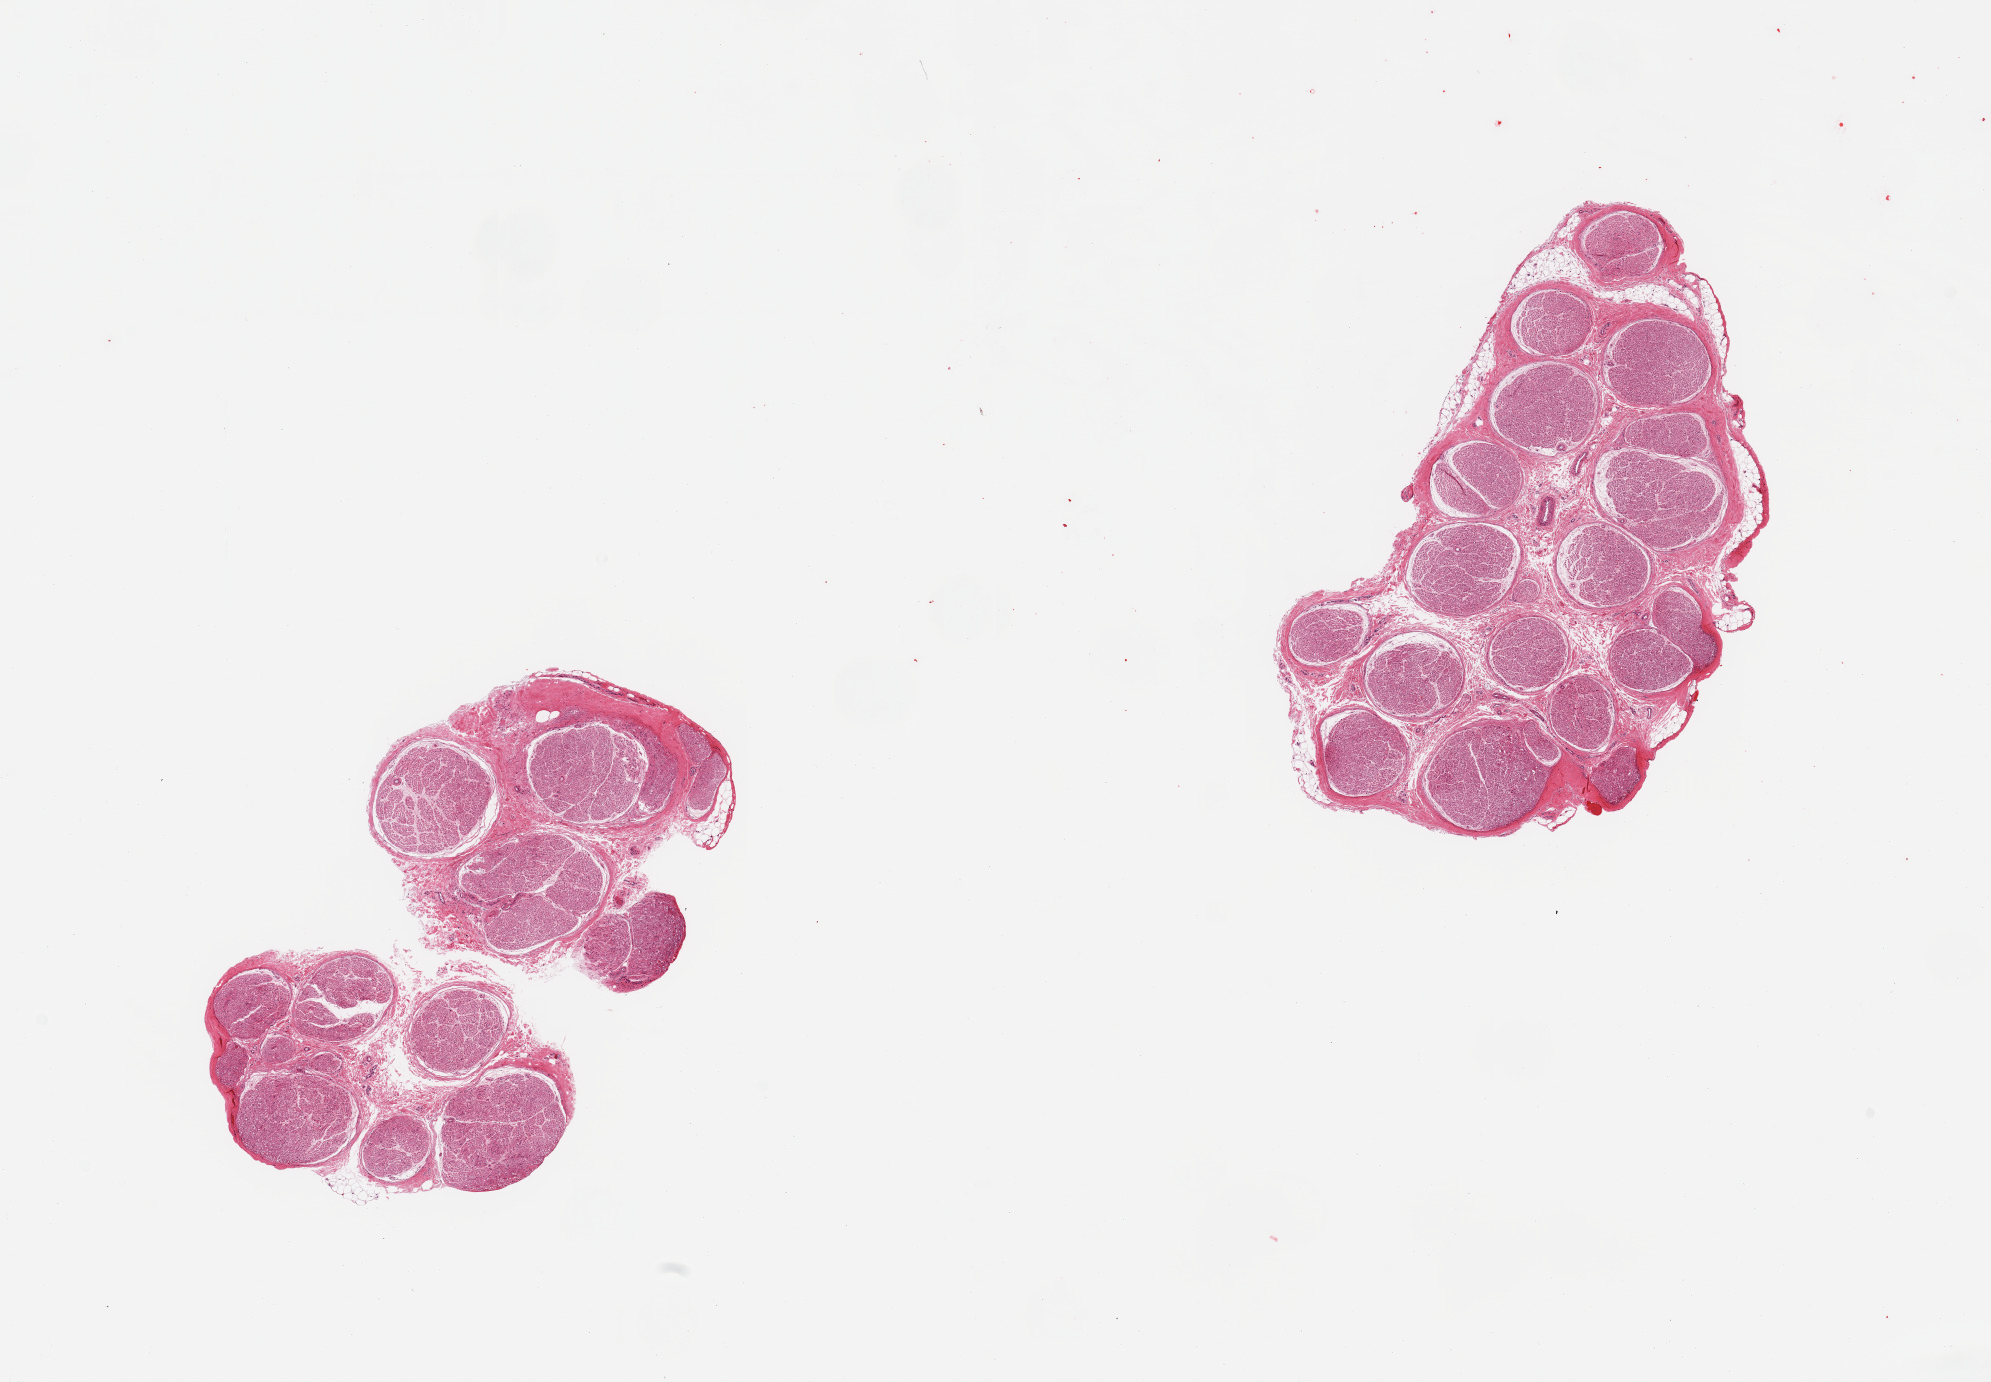
Digitized H&E-stained section, shown as a low-resolution overview of the whole scanned area (about 15.8 x 10.9 mm, from a 20x scan). PAXgene-fixed paraffin-embedded (PFPE) section. Section of tibial nerve (target tissue). Tissue donor sample. Female donor.
Review note (as recorded): 2 pieces; well dissected; 10% internal fibrofatty content.